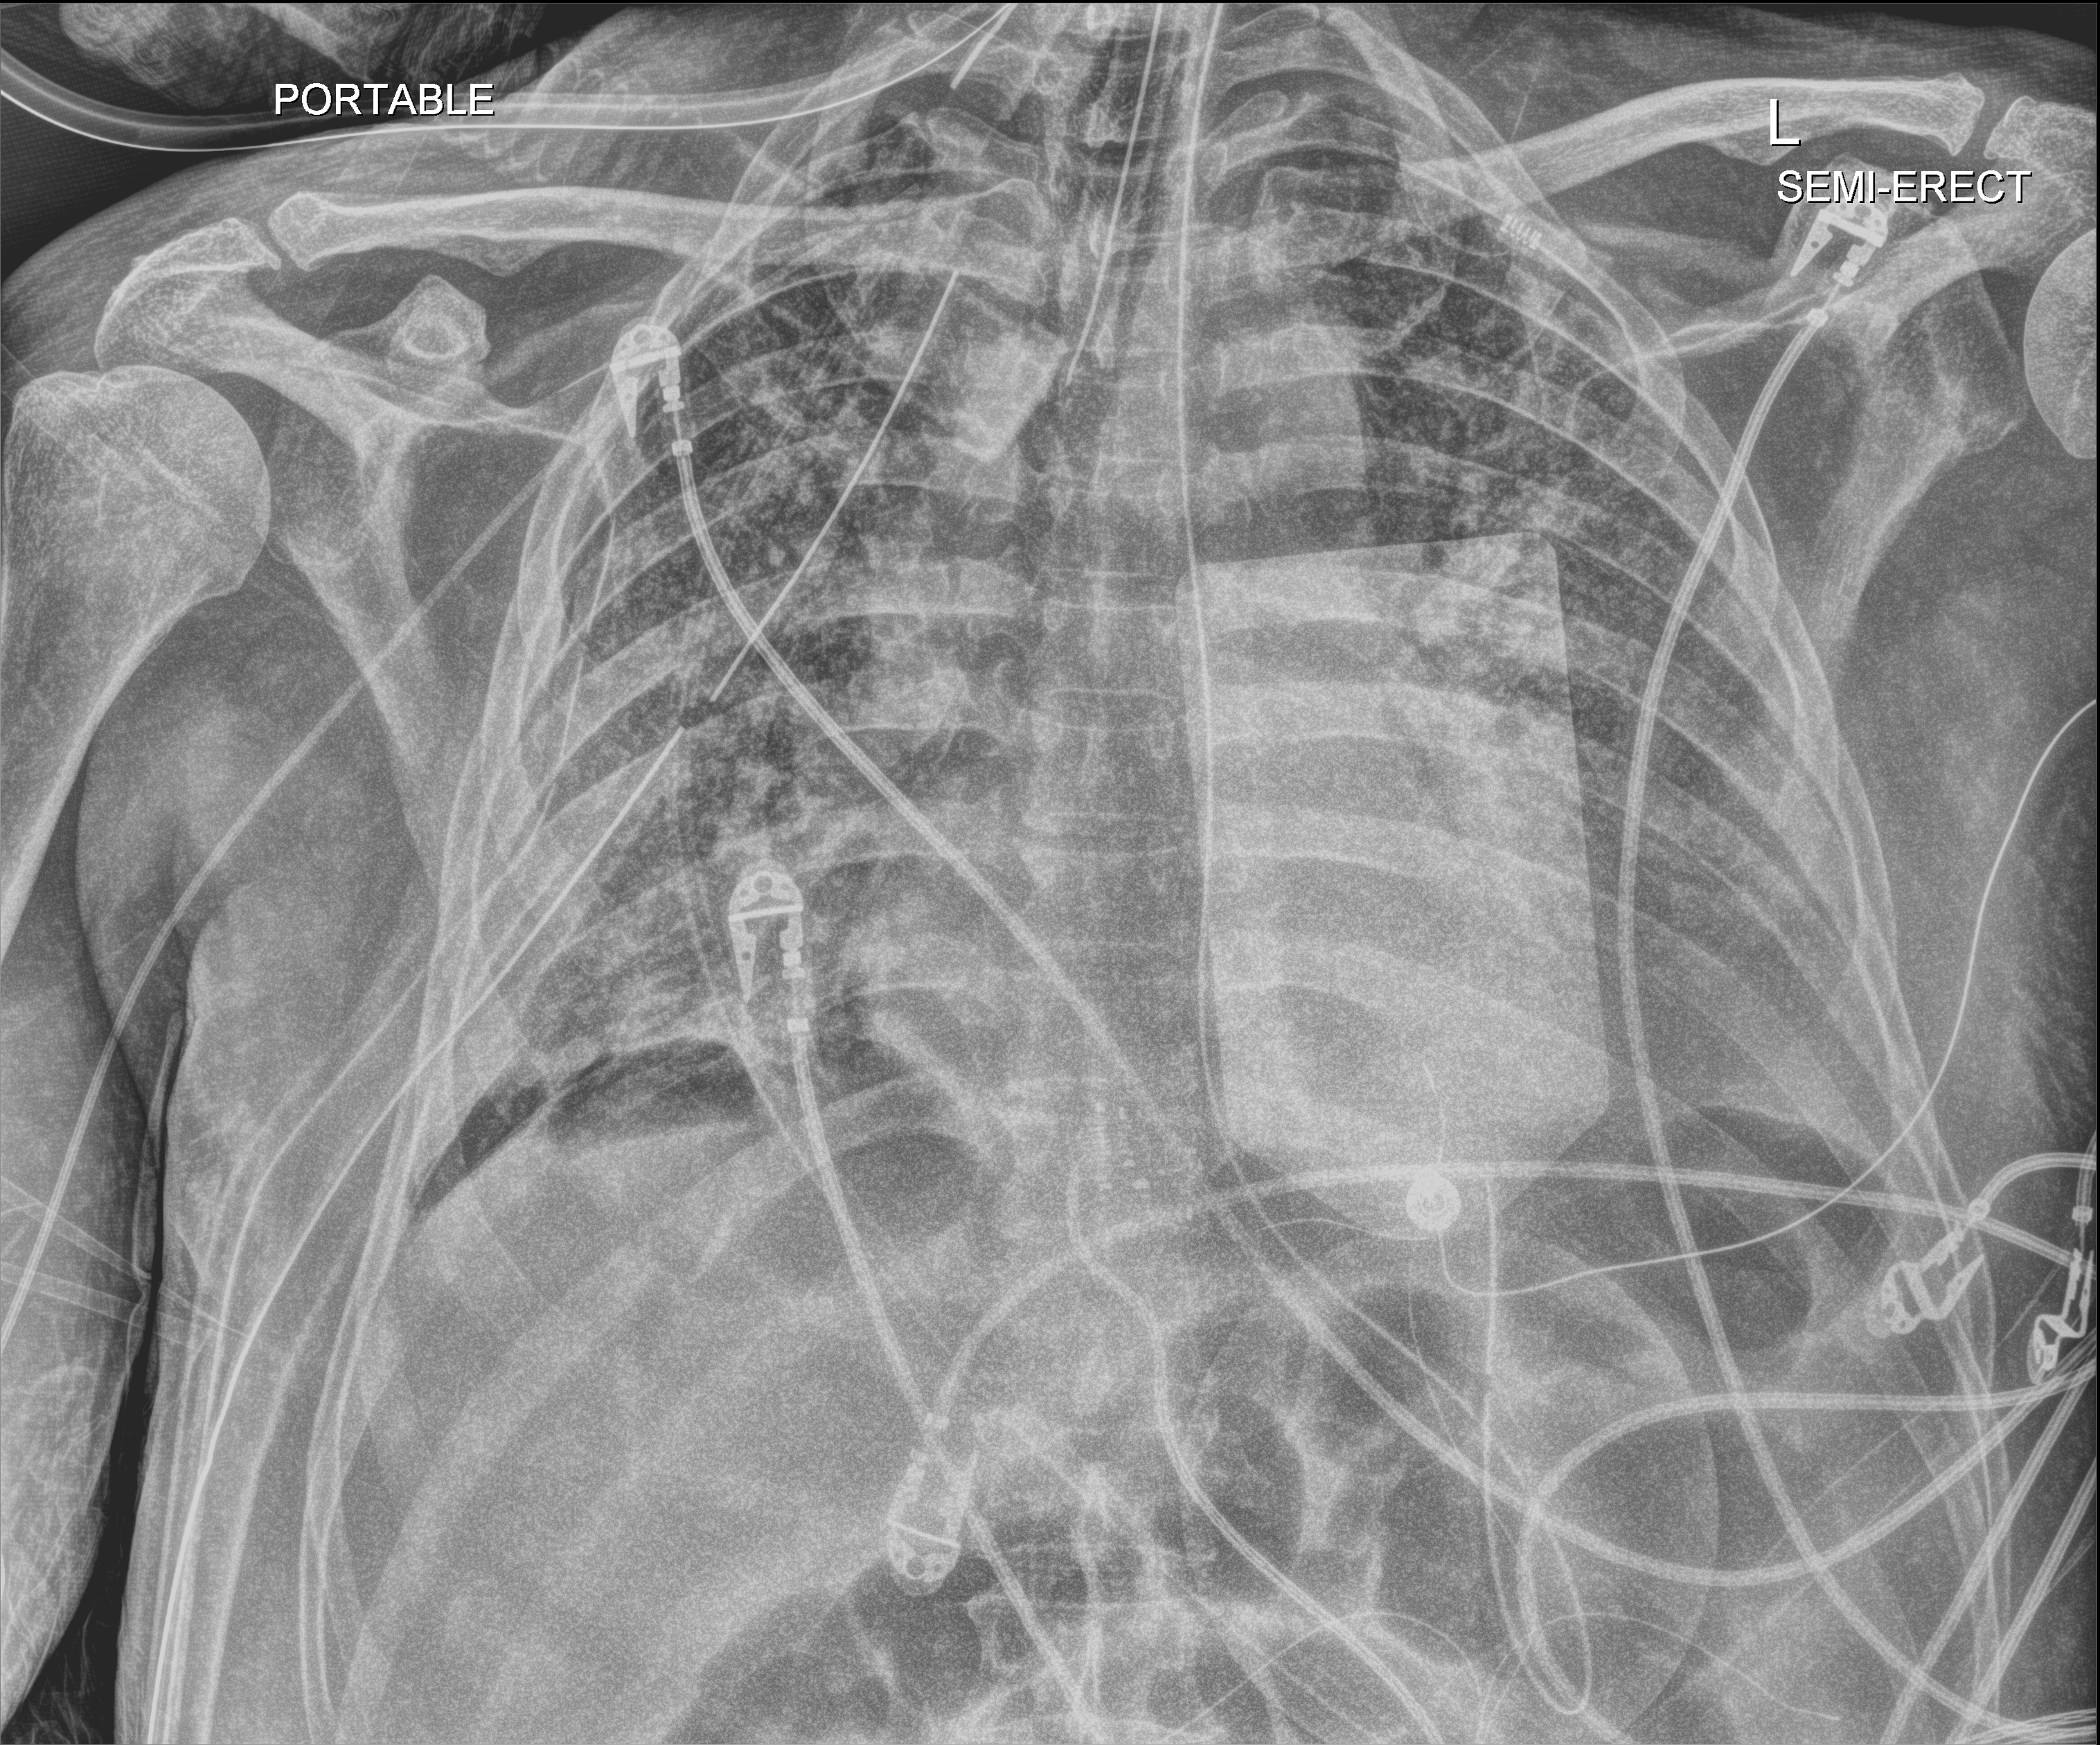
Chest X-ray (portable), anteroposterior (AP) projection. Male patient hospitalised with COVID-19, age 60–74 years.
From the hospital-stay record, not from the radiograph (when in the stay this image was taken is not recorded): smoking status (admission record): never; mechanically ventilated during this hospital stay: yes.